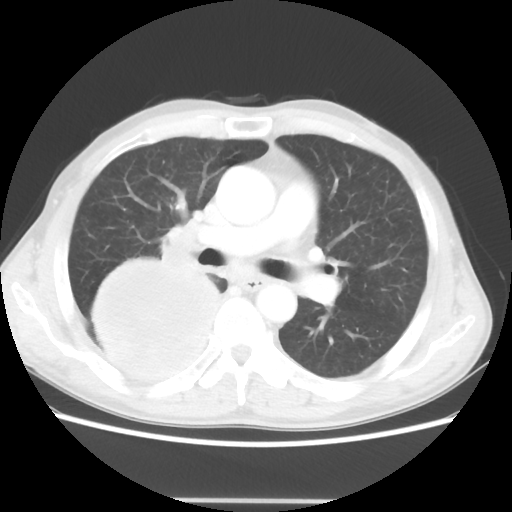
Chest CT, one axial slice; position 28 of 48 along the scan axis; 100 kVp; lung window (W 1500 / L -600 HU); 512 × 512 image matrix, field of view 361 × 361 mm. Patient: male, 66 years. Case-level facts recorded for this patient, not image findings: clinical TNM (as recorded): T4 N1 M1; histopathological grade: G3.
Structures marked on this image (bounding box drawn by a radiologist):
- lung tumour (recorded histology: small cell carcinoma): bounding box [x1, y1, x2, y2] px = [77, 248, 221, 394]